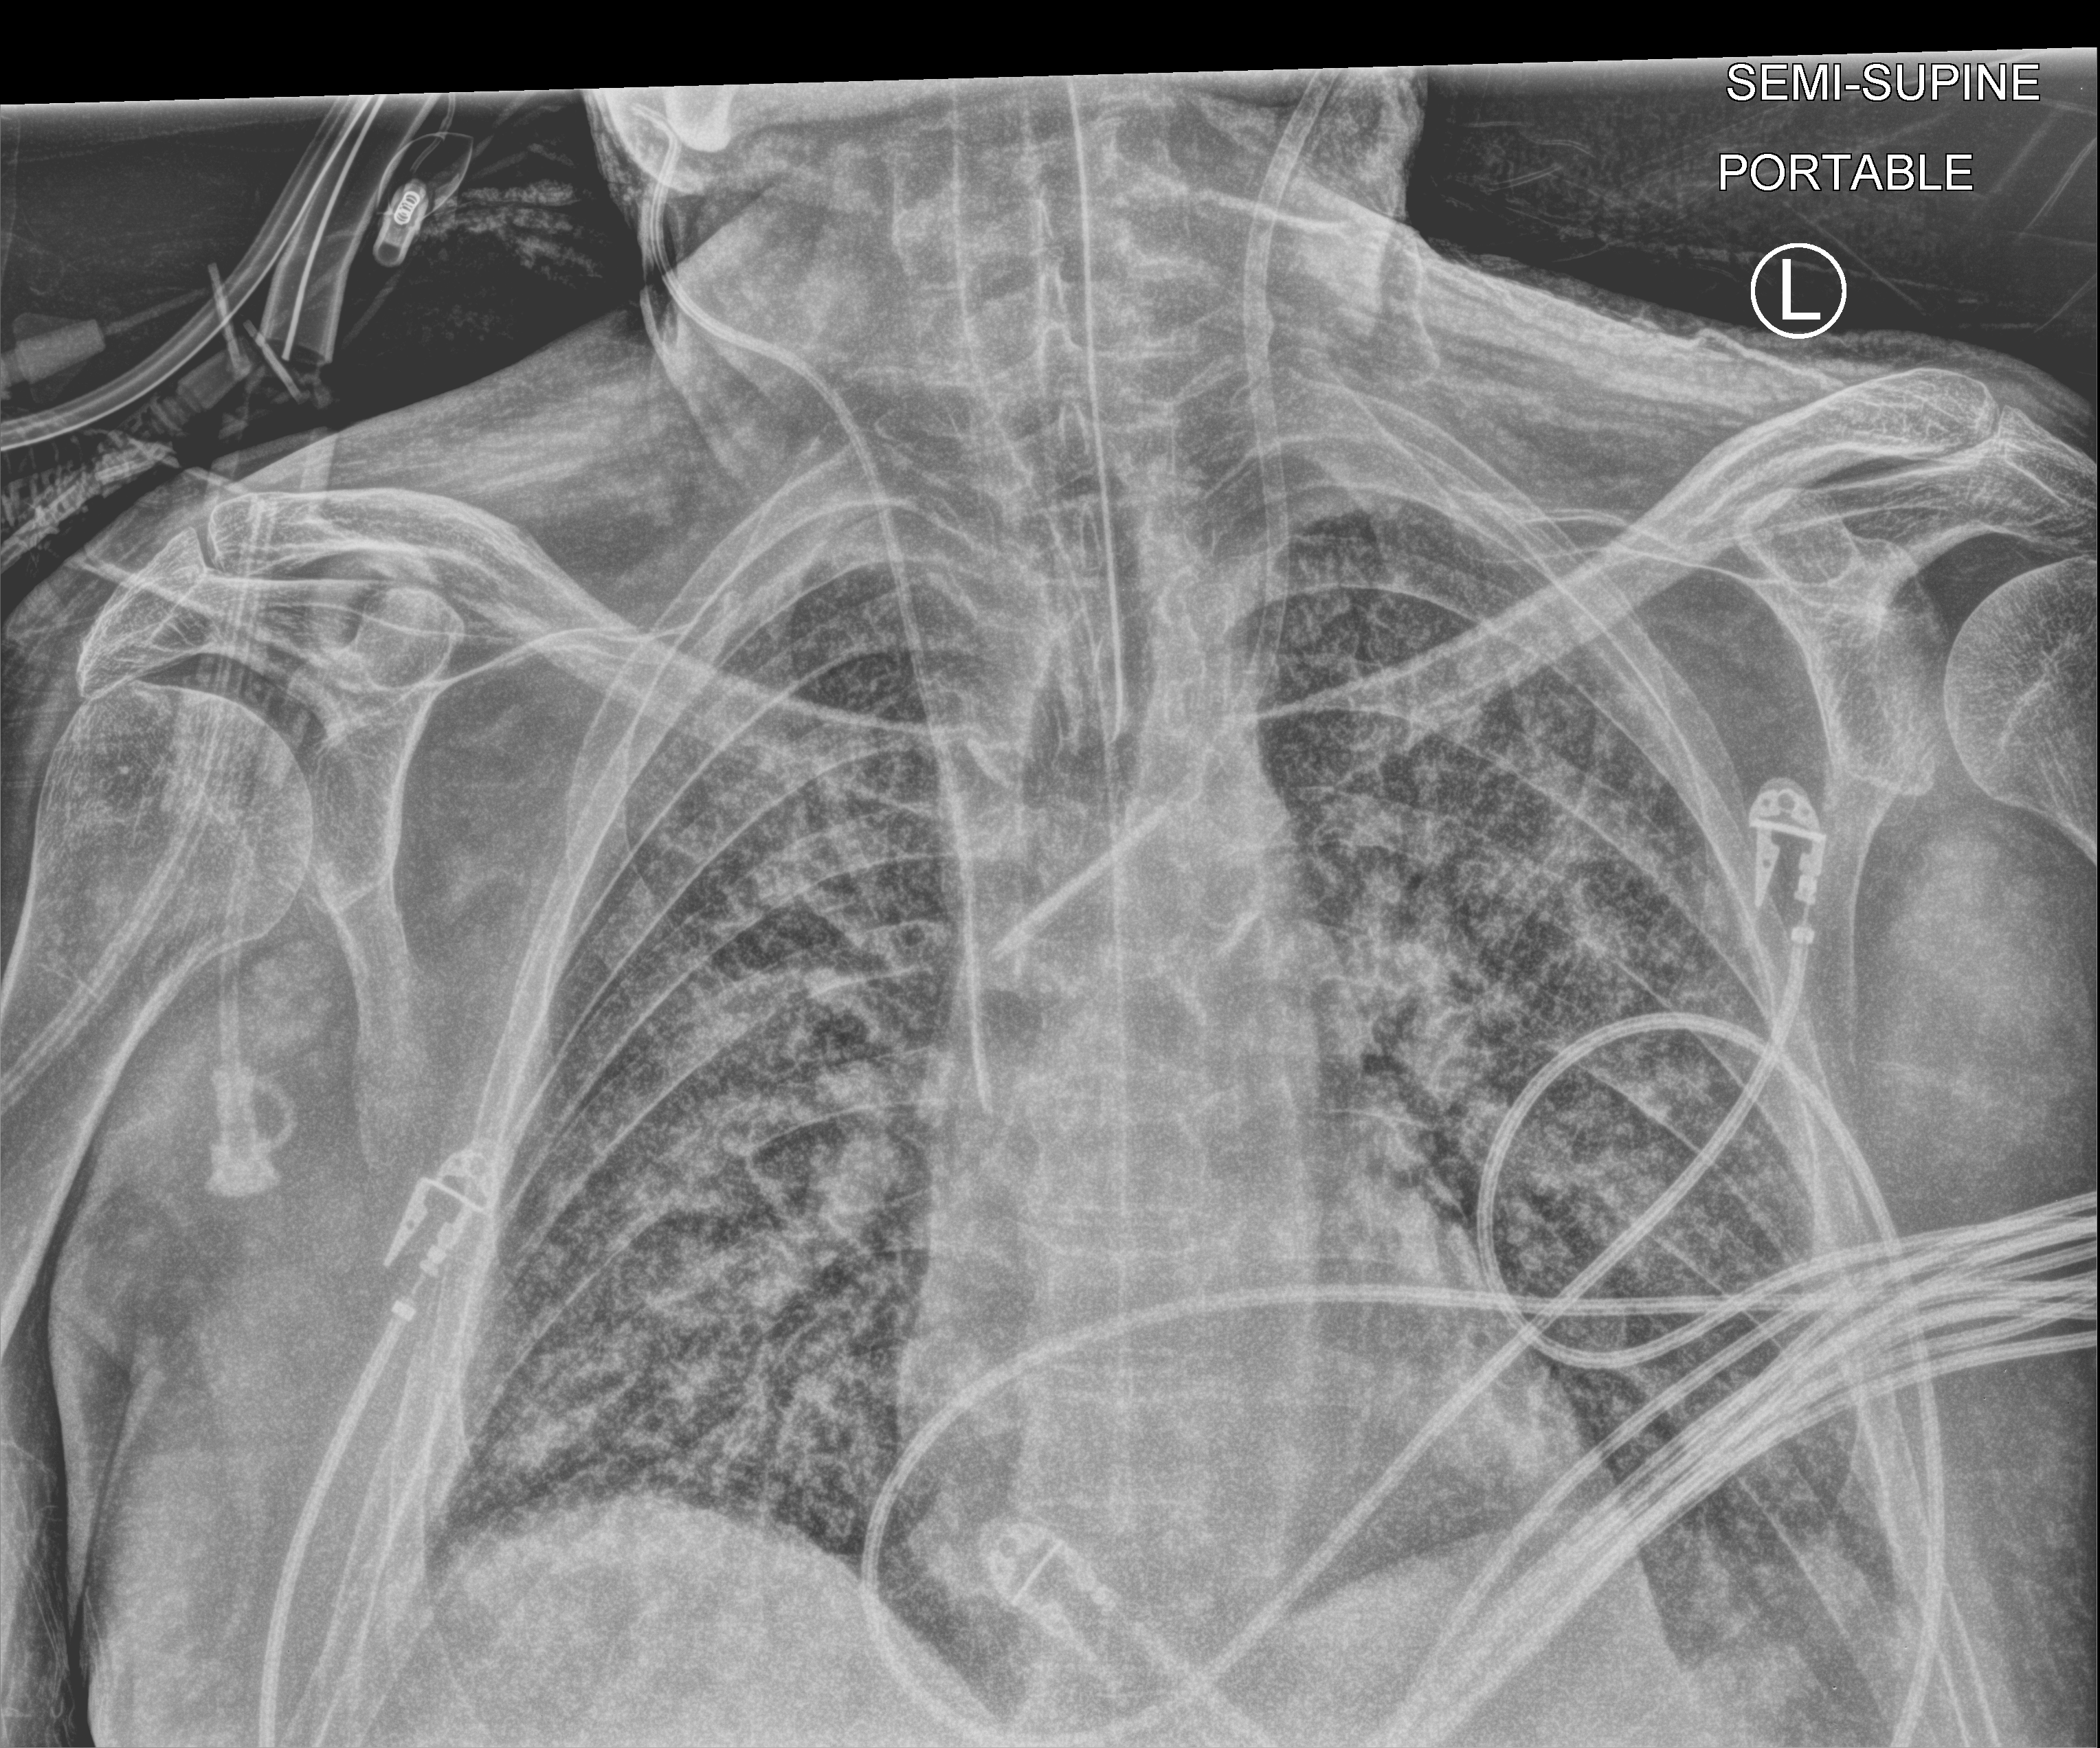
Chest X-ray (portable), anteroposterior (AP) projection. Male patient hospitalised with COVID-19, age 60–74 years.
Admission-level facts for this patient (not findings on this image; timing relative to this image not recorded): smoking status (admission record): never; mechanically ventilated during this hospital stay: yes.